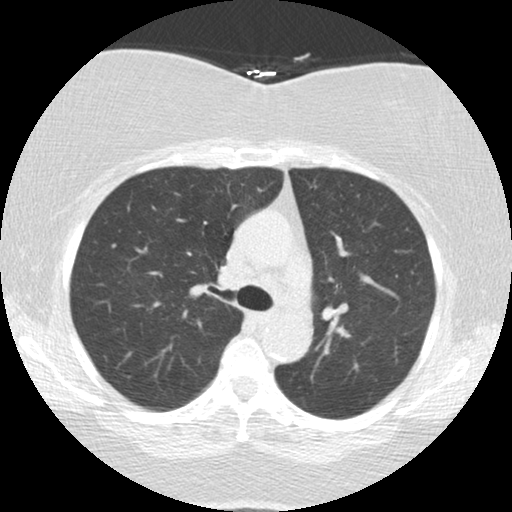
Low-dose screening chest CT, one axial slice; reconstruction kernel STANDARD; 120 kVp; lung window (W 1500 / L -600 HU); 2.5 mm slice thickness; 512 × 512 image matrix.
Annotated regions visible in this slice (outlined manually by an expert reader):
- lesion 1 (tumor, lower lobe of left lung): box from (x=218, y=266) to (x=245, y=286) px